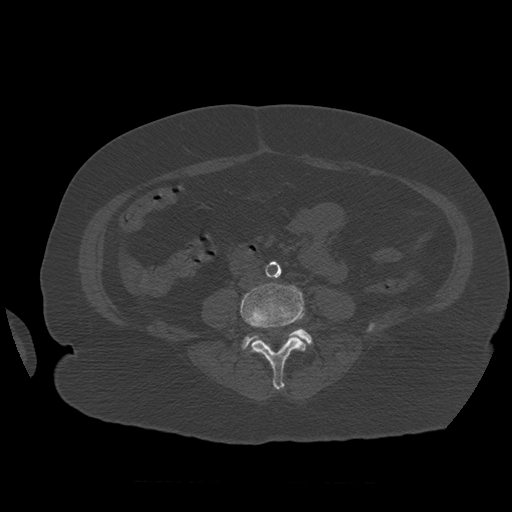
CT including the spine, one axial slice; slice 199 of 399 in the series (ordered by position); reconstruction kernel STANDARD; 120 kVp; bone window (W 1800 / L 400 HU); 512 × 512 image matrix, field of view 404 × 404 mm. Patient age 81 years. From the clinical record (not read from this slice): primary cancer: renal; vertebrae with lytic lesions (as recorded): L1.
Structures marked on this image (semi-automatically segmented with operator editing):
- L4 vertebra: bounding box <240,284,307,390> (left, top, right, bottom; pixels)
- L5 vertebra: <242,329,313,349>